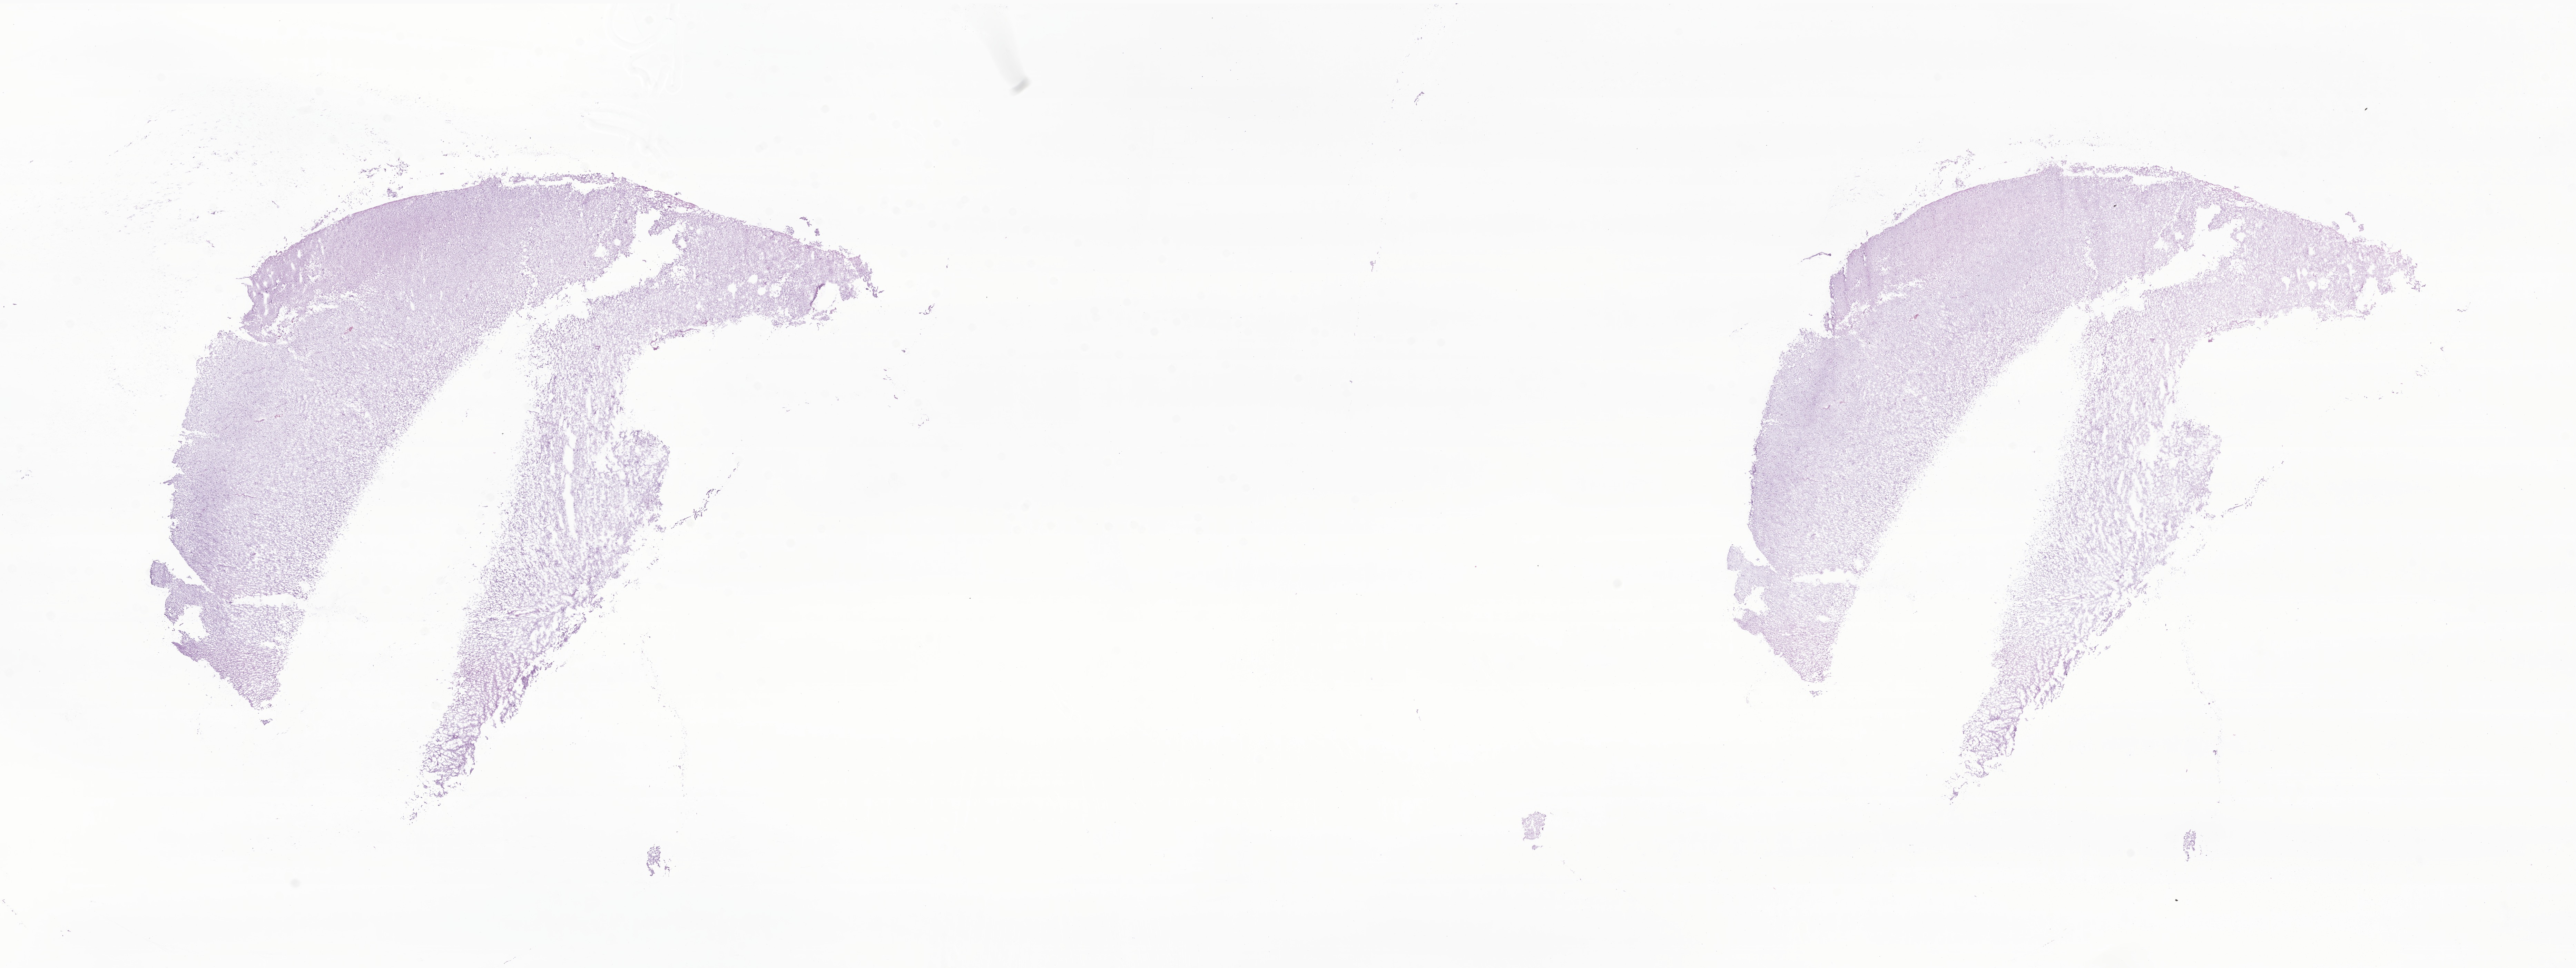
H&E whole-slide image of tumor tissue from the brain — low-resolution overview of the scanned area, about 31.5 x 11.8 mm, cryosection (OCT / tissue freezing medium). Patient male; age 91 months (7 years 7 months).
- diagnosis (ICD-O-3 morphology term): Dysembryoplastic neuroepithelial tumor